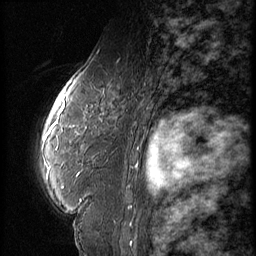
Breast MRI (dynamic contrast-enhanced), one sagittal slice. Position 40 of 56 along the scan axis. Dynamic contrast-enhanced series, image 2 of 3 at this slice position (ordered by acquisition). 1.5 T. TE 4.2 ms, TR 9 ms. 2.5 mm slice thickness. 256 × 256 image matrix. Female patient, age 59 years. Case-level facts recorded for this patient, not image findings: setting: breast cancer imaged before/during neoadjuvant chemotherapy; receptor status: HER2-positive.
Structures marked on this image (semi-automatically segmented with operator editing):
- analysis volume of interest (the breast-tissue region the enhancement analysis was run in; not a lesion): bounding box (x1, y1, x2, y2) in pixels: (44, 66, 151, 135)
- tumour enhancement mask (voxels above the 140 % enhancement threshold inside the analysis volume of interest): (46, 91, 66, 135)